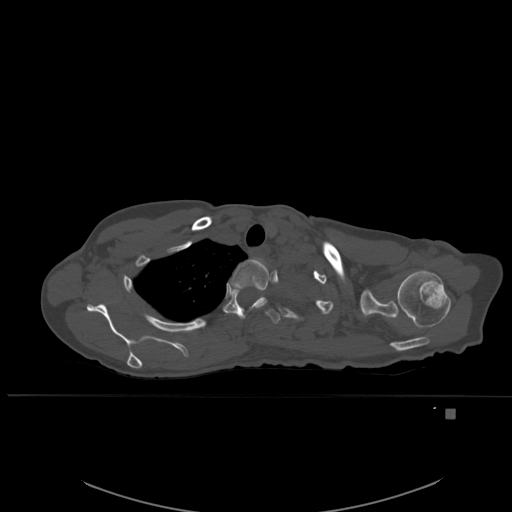
CT including the spine, one axial slice; slice 430 of 537 in the series (ordered by position); bone window (W 1800 / L 400 HU); 1.5 mm slice thickness; 512 × 512 image matrix. Patient: female, 45 years. Case-level facts recorded for this patient, not image findings: primary cancer: lung.
Structures marked on this image (semi-automatic segmentation, software-assisted and operator-edited):
- T2 vertebra: bounding box [x1, y1, x2, y2] px = [231, 258, 270, 311]
- T3 vertebra: [223, 288, 280, 324]